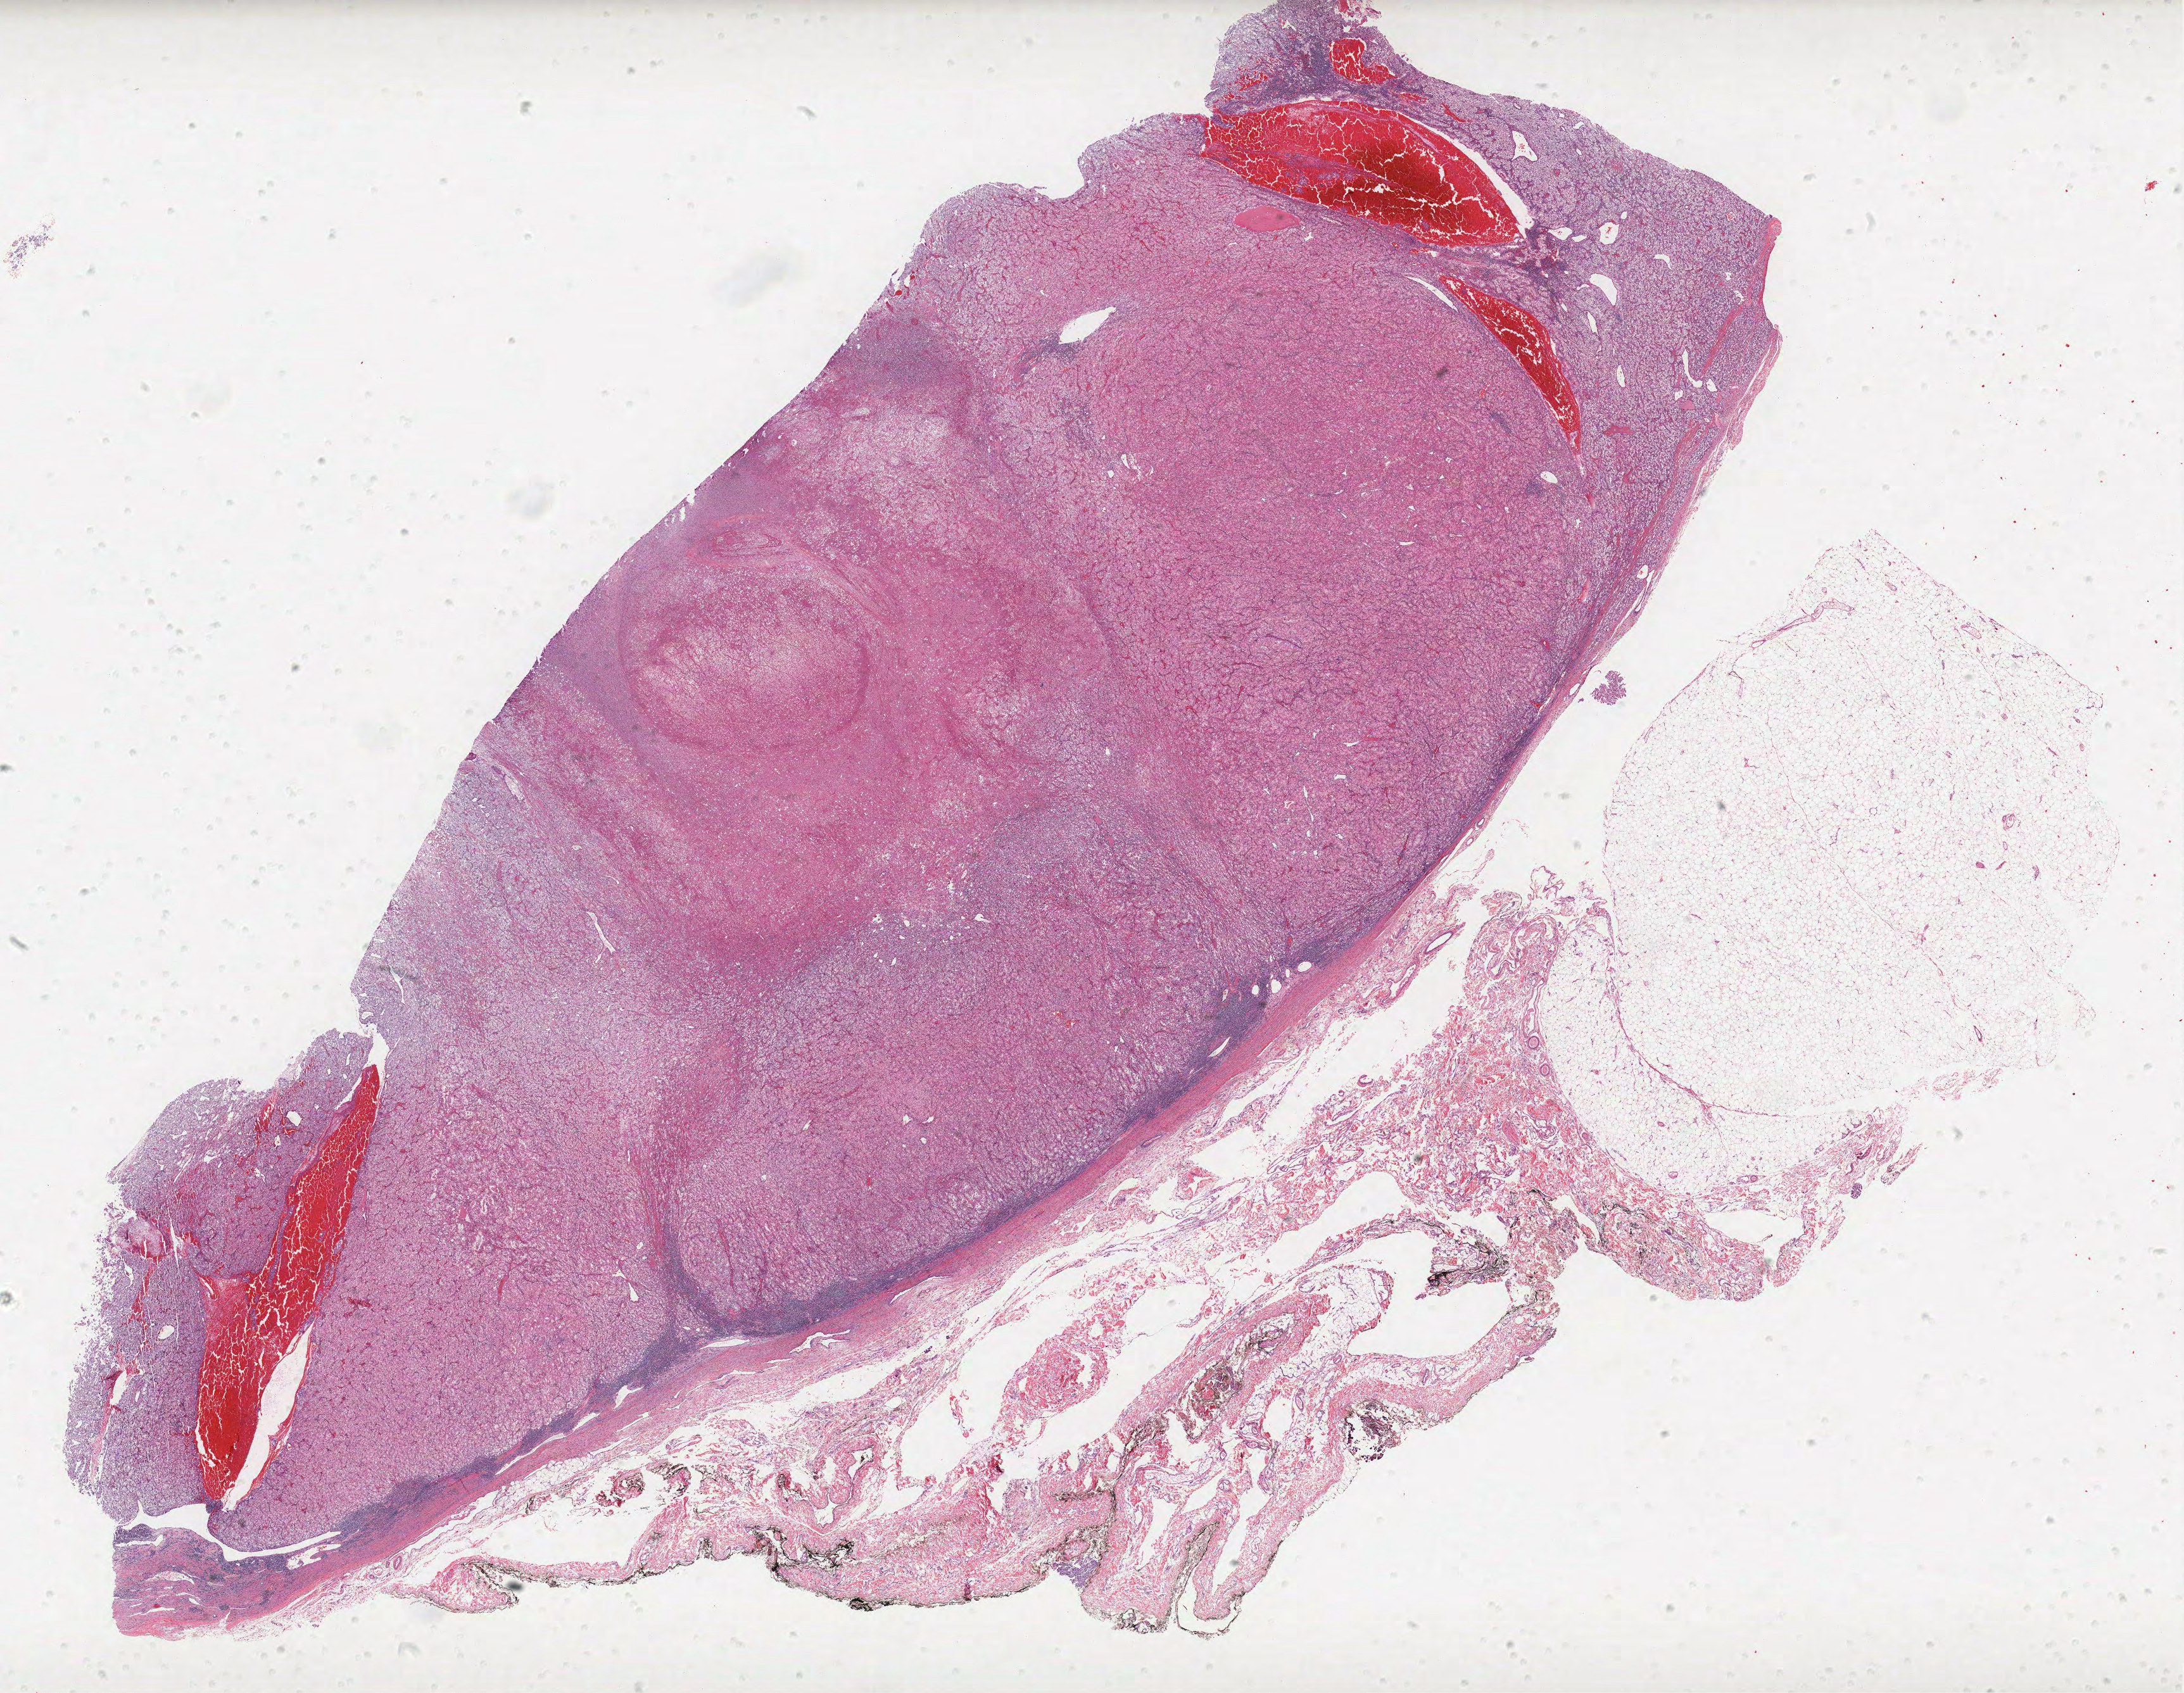
Digitized Hematoxylin and eosin (H&E) stained tissue section (whole slide), low-resolution overview of the scanned area, about 27.6 x 21.4 mm; FFPE section; sample: primary tumour, kidney. Female patient; age at initial diagnosis 75 years. Histologic grade: G2 (moderately differentiated).
TNM: T2 N0 M0. Diagnosis: Clear cell adenocarcinoma, NOS. AJCC pathologic stage: II. Laterality: right.